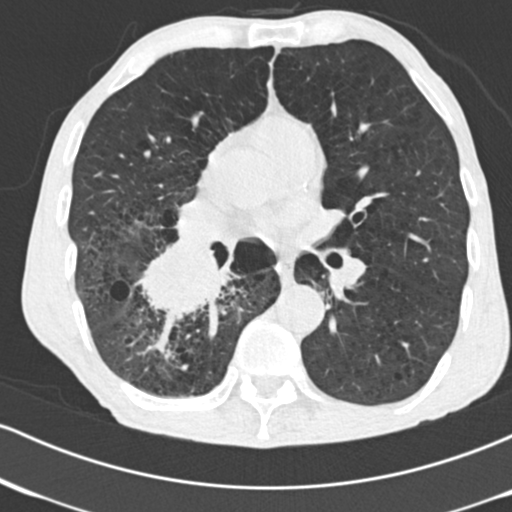
Low-dose screening chest CT, axial slice. Second screening round (one year after baseline). Lung window (W 1500 / L -600 HU). 2 mm slice thickness. 120 kVp. 512 × 512 image matrix. Male, age 64 years at enrolment. Current smoker at enrolment.
Expert-annotated lung lesion, bounding box [x1, y1, x2, y2] px = [128, 228, 240, 333]. Reader record for this screening exam (exam-level; its link to the box is not recorded): non-calcified nodule or mass ≥4 mm, 52 × 37 mm, spiculated (stellate) margins, soft tissue attenuation, pre-existing on the prior screen: no. Official screen result: positive, other. Lung cancer was diagnosed 28 days after this screen: adenocarcinoma, NOS, right lower lobe, stage IV (AJCC 6th edition), 60 mm at pathology.